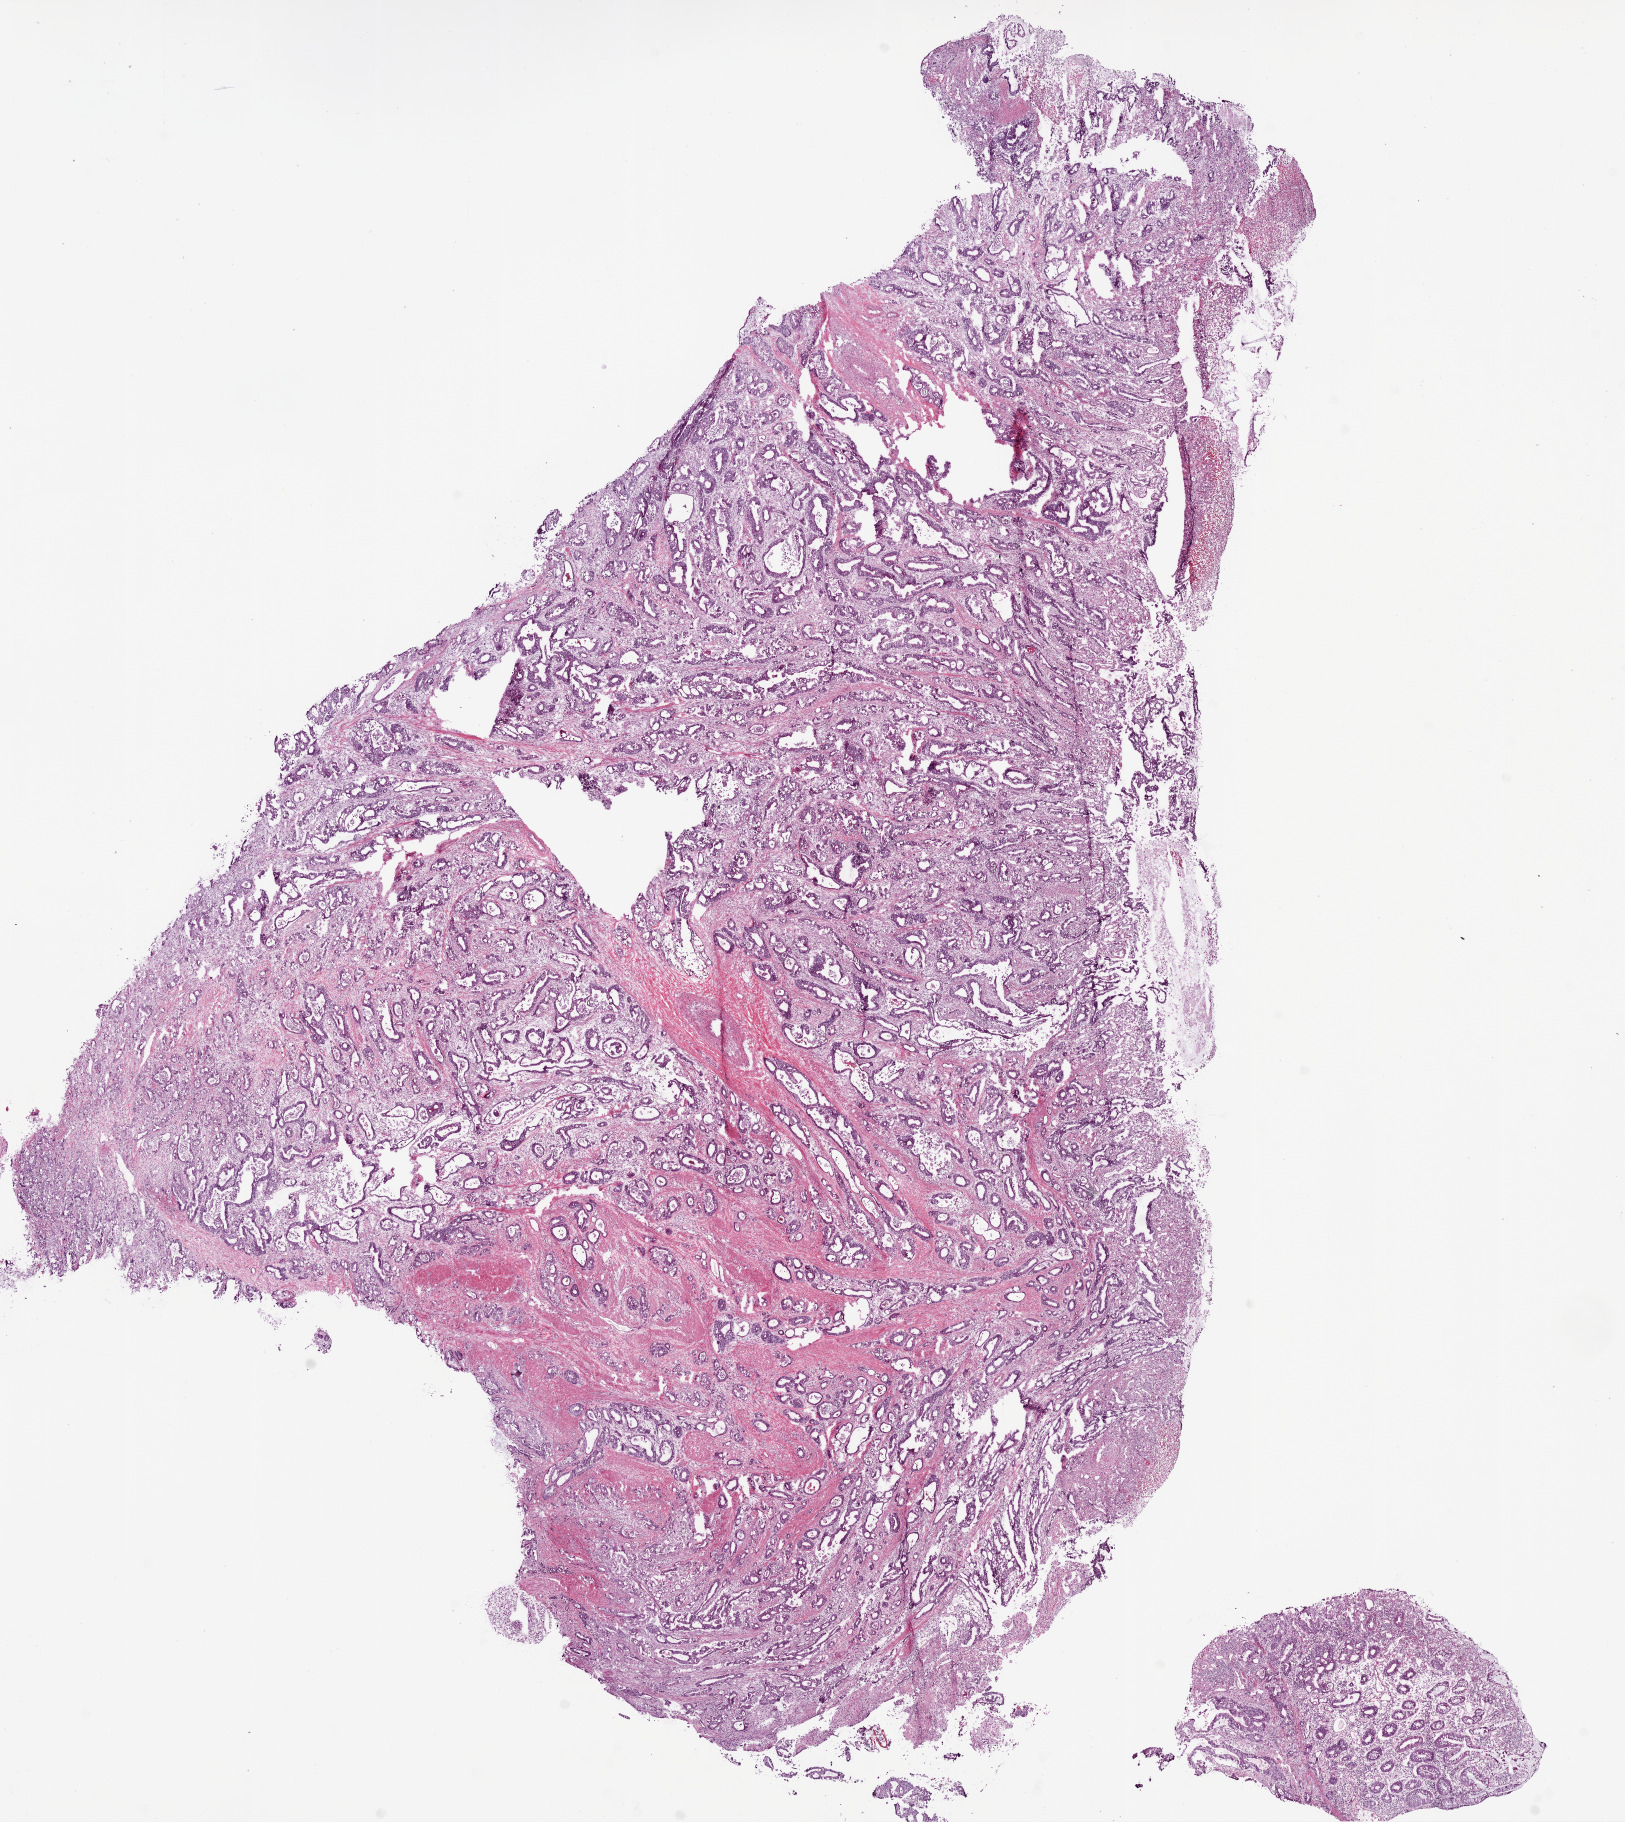
Whole-slide histology image, H&E-stained, shown as a low-resolution overview of the whole scanned area (about 13.0 x 14.6 mm, from a 20x scan). Frozen section. Colon, primary tumour sample. Patient: male, age at initial diagnosis 72 years. Slide review estimates, as recorded: tumour cells 95%, tumour nuclei 70%, normal cells 4%, stromal cells 0%, necrosis 1%. Inflammatory infiltration, as recorded: lymphocyte infiltration 10%, monocyte infiltration 5%, neutrophil infiltration 2%.
• AJCC pathologic stage: IIIB (7th edition)
• lymph nodes positive (case pathology): 1 of 19 examined
• diagnosis: Adenocarcinoma, NOS (cecum)